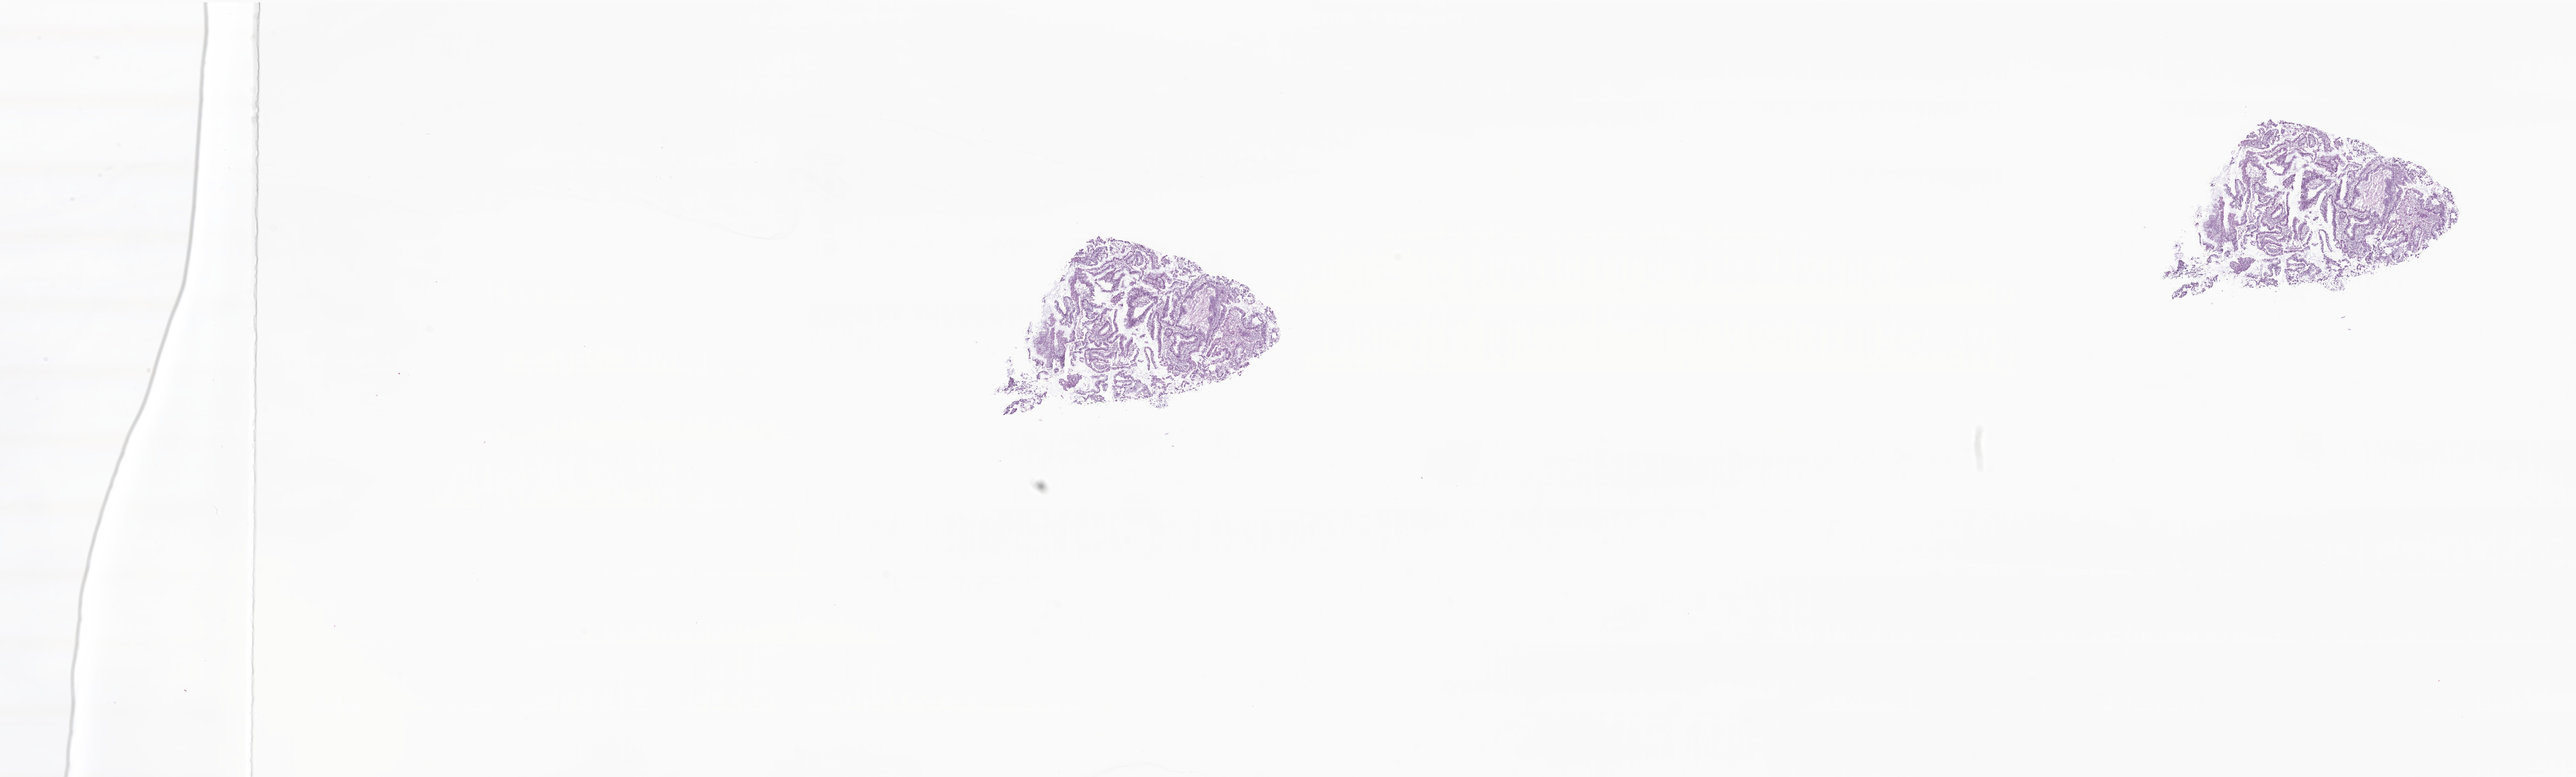
Digitized H&E-stained section — low-resolution overview of the scanned area, about 40.6 x 12.2 mm, cryosection, specimen: primary tumor, anatomic site: rectosigmoid junction. Female patient. Tumor grade: G1 (well differentiated). Pathologist review of this section (percent, as recorded): tumor cells 60%, tumor nuclei 60%, stromal cells 40%, necrosis 0%, normal cells 0%. Infiltration values recorded for this section: lymphocyte infiltration 100%, monocyte infiltration 0%, neutrophil infiltration 0%.
AJCC pathologic stage: Stage I. Diagnosis: Adenocarcinoma, NOS.